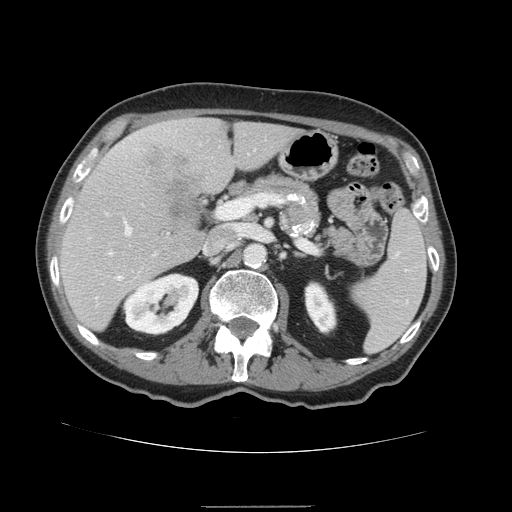
Contrast-enhanced abdominal CT, one axial slice. Slice 84 of 168 in the series (ordered by position). Soft-tissue window (W 400 / L 40 HU). 512 × 512 image matrix. Male patient, age 74 years. From the clinical record (not read from this slice): diagnosis: colorectal cancer liver metastases, imaged before liver resection; multiple liver metastases: no; largest metastasis: 14.5 cm; disease in both lobes: yes.
Annotated regions visible in this slice (outlined manually by an expert reader):
- hepatic veins: bounding box <119,222,132,278> (left, top, right, bottom; pixels)
- liver: <59,118,304,332>
- planned liver remnant (the part of the liver to remain after resection): <59,122,303,332>
- portal vein (with intrahepatic branches): <106,201,240,268>
- liver metastasis: <140,143,207,227>